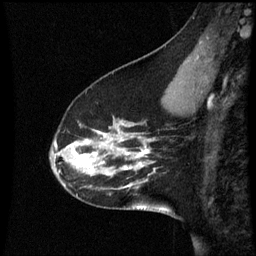
Breast MRI (dynamic contrast-enhanced), one sagittal slice. Position 17 of 60 along the scan axis. Dynamic contrast-enhanced series, image 2 of 3 at this slice position (ordered by acquisition). 1.5 T. TE 4.2 ms, TR 8.9 ms. 2 mm slice thickness. 256 × 256 image matrix, field of view 200 × 200 mm. Female patient, age 45 years. Case-level facts recorded for this patient, not image findings: setting: breast cancer imaged before/during neoadjuvant chemotherapy; receptor status: HR-positive, HER2-negative.
Outlined on this slice (semi-automatic segmentation, software-assisted and operator-edited):
- analysis volume of interest (the breast-tissue region the enhancement analysis was run in; not a lesion): box from (x=50, y=94) to (x=171, y=205) px
- tumour enhancement mask (voxels above the 70 % enhancement threshold inside the analysis volume of interest): (x=72, y=130)–(x=149, y=175)